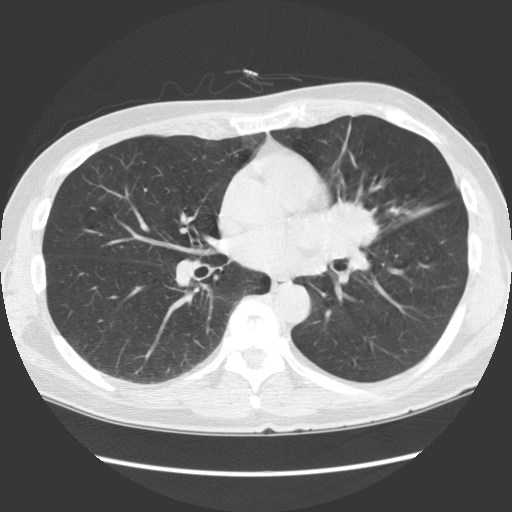
Chest CT (low-dose screening protocol), one axial image; baseline screening round; lung window (W 1500 / L -600 HU); standard (soft-tissue) reconstruction kernel (STANDARD); 140 kVp. Male, age 61 years at enrolment.
Expert-annotated lung lesion, bounding box <304,184,399,284> (left, top, right, bottom; pixels). Reader record for this screening exam (exam-level; its link to the box is not recorded): non-calcified nodule or mass ≥4 mm, lingula, 35 × 35 mm, spiculated (stellate) margins, soft tissue attenuation.